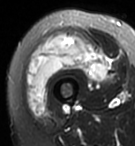
MRI of an extremity soft-tissue mass, one axial slice. Slice 30 of 95 in the series (ordered by position). T2-weighted fat-saturated. MR volume resampled by the dataset authors to the PET/CT grid (not the native acquisition matrix). 3.27 mm slice thickness. 135 × 146 image matrix, field of view 132 × 143 mm. Female patient. From the clinical record (not read from this slice): histological type: pleiomorphic undifferentiated sarcoma; grade: high; site of the primary tumour: right quadricep.
Annotated regions visible in this slice (expert contour drawn on MRI and transferred to this co-registered scan by the dataset authors):
- gross tumour volume including surrounding oedema: box from (x=25, y=34) to (x=109, y=117) px
- gross tumour volume (mass): (x=25, y=34)–(x=109, y=117)